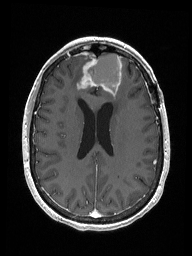
Brain MRI from a brain-tumour surgery series, one axial slice. Position 68 of 192 along the scan axis. T1-weighted post-contrast. 1 mm slice thickness. 192 × 256 image matrix, field of view 187 × 250 mm. Case-level facts recorded for this patient, not image findings: histopathology: Metastastic Carcinoma from Breast primary.
Annotated regions visible in this slice (expert manual segmentation):
- previous resection cavity: box from (x=87, y=53) to (x=122, y=95) px